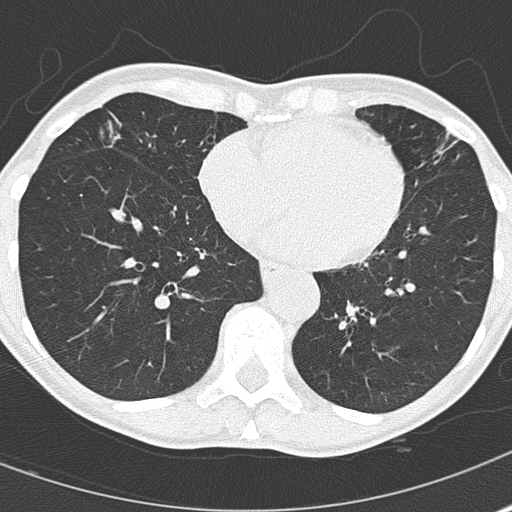
Axial slice from a low-dose chest CT screening exam; second annual screen; lung window (W 1500 / L -600 HU); 2 mm slice thickness. Female participant, aged 67 years at enrolment. Current smoker at enrolment.
Lesion marked by an expert reader, bounding box <83,102,196,193> (left, top, right, bottom; pixels). The screening reader recorded 2 non-calcified nodules or masses ≥4 mm on this exam (right middle lobe, right middle lobe); which of them this box marks is not recorded. Later outcome: lung cancer diagnosed 475 days after this screen (after the third annual screen) — bronchiolo-alveolar adenocarcinoma, NOS, right middle lobe, well differentiated (G1), stage IA (AJCC 6th edition), 25 mm at pathology.